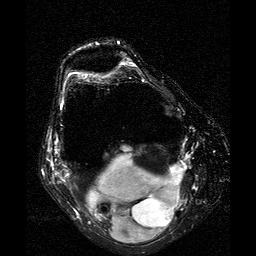
MRI of an extremity soft-tissue mass, one axial slice; slice 12 of 25 in the series (ordered by position); T2-weighted fat-saturated; 256 × 256 image matrix, field of view 160 × 160 mm. Female patient. From the clinical record (not read from this slice): histological type: liposarcoma; site of the primary tumour: right thigh.
Annotated regions visible in this slice (outlined manually by an expert reader):
- gross tumour volume (mass): box from (x=84, y=154) to (x=186, y=245) px